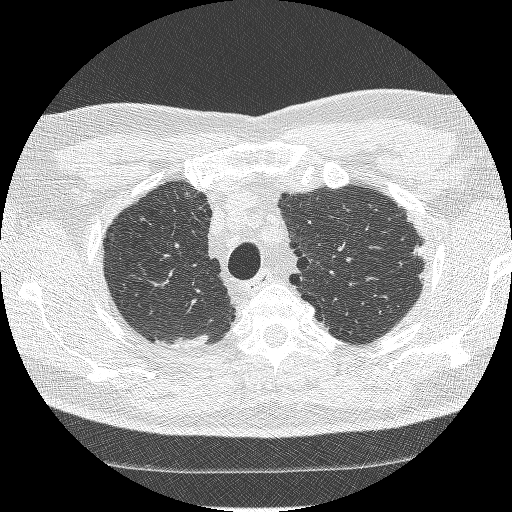
Chest CT (low-dose screening protocol), one axial image; baseline screening round; lung window (W 1500 / L -600 HU); lung (sharp) reconstruction kernel (BONE); slice 224 of 260 in the series. Male participant, aged 66 years at enrolment. Current smoker at enrolment.
Expert-annotated lung lesion, bounding box (x1, y1, x2, y2) in pixels: (398, 233, 434, 268). The exam's reader record, not a measurement of the box and not confirmed to be the same lesion: non-calcified nodule or mass ≥4 mm, right lower lobe, 45 × 19 mm, spiculated (stellate) margins, soft tissue attenuation. Note: the box lies in the patient's left hemithorax on this image, whereas the reader's record names the right lung; they may be different findings.